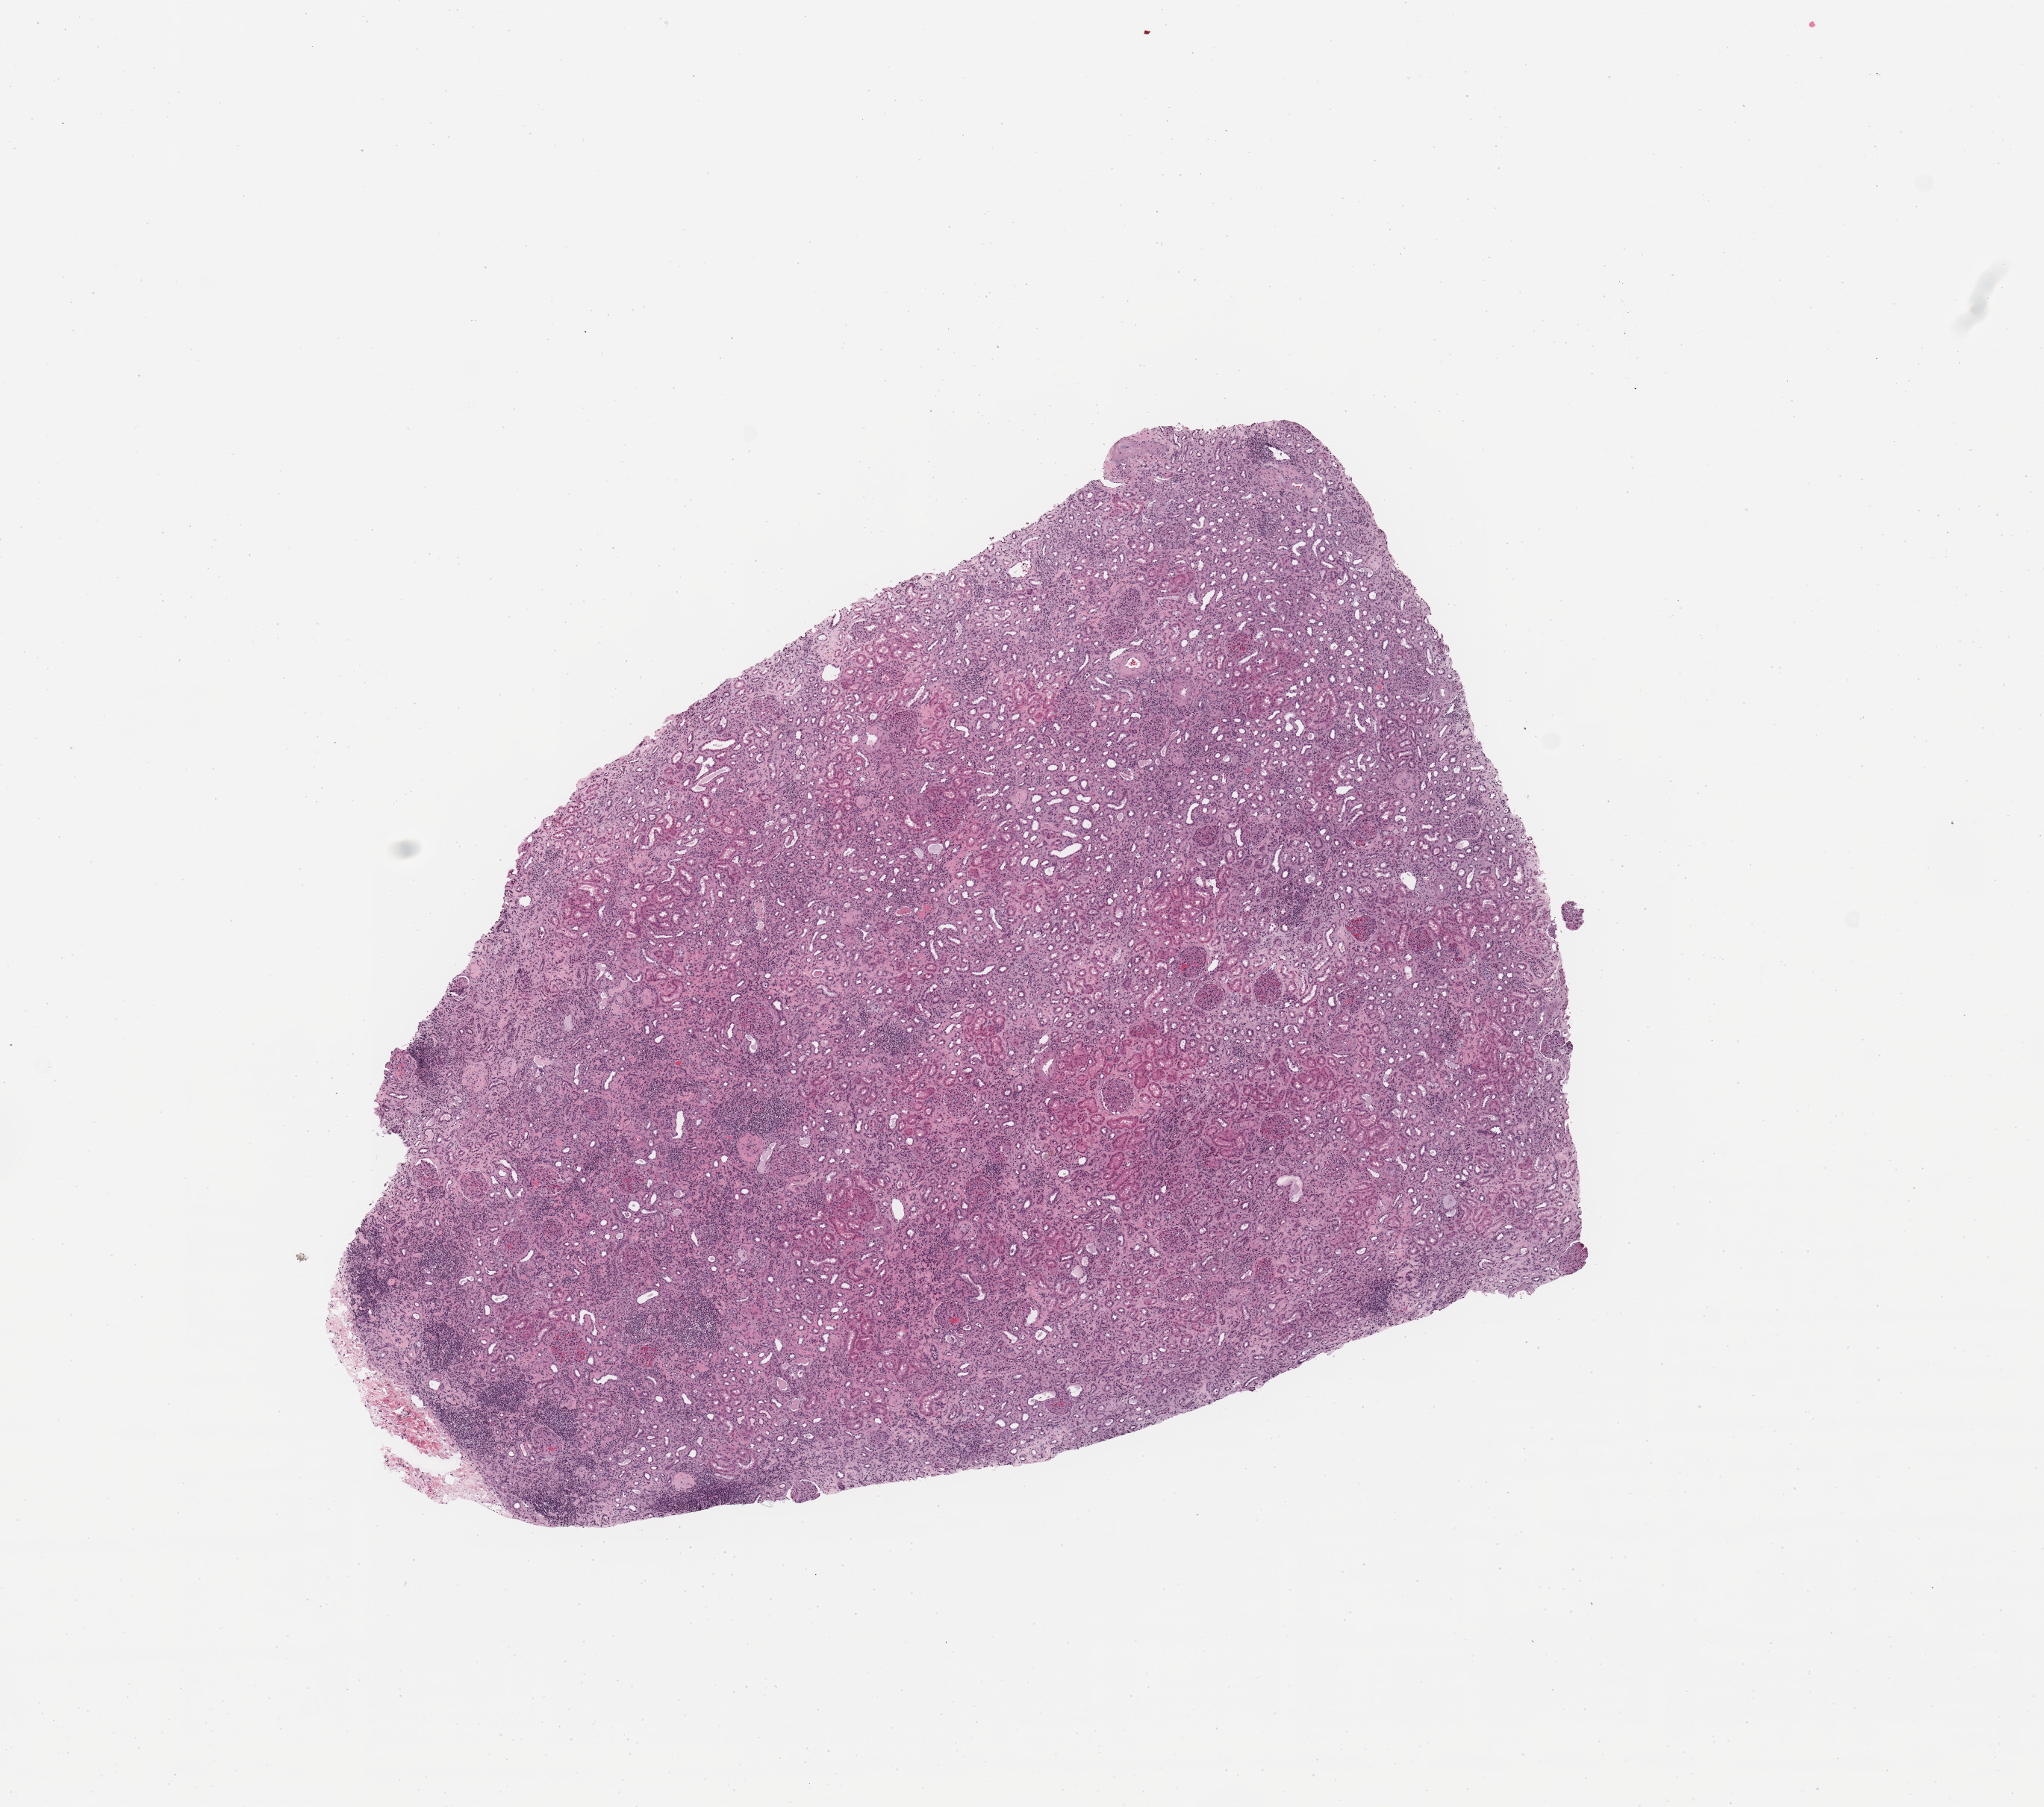
Digitized Hematoxylin and eosin (H&E) stained tissue section (whole slide) — low-resolution overview of the scanned area, about 10.8 x 9.6 mm (slide scanned at 20x); normal (non-tumour) tissue sample, sampled site: kidney. Male, 83 y/o.
This section: normal (non-tumour) tissue from the same patient. Patient diagnosis: Renal cell carcinoma, NOS.